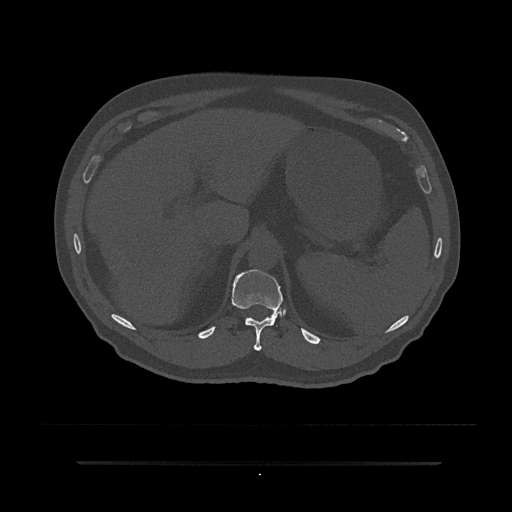
CT including the spine, one axial slice. Slice 260 of 797 in the series (ordered by position). Reconstruction kernel Br40s/3. 120 kVp. Bone window (W 1800 / L 400 HU). 512 × 512 image matrix, field of view 464 × 464 mm. Male patient, age 59 years. Case-level facts recorded for this patient, not image findings: primary cancer: bile ducts; vertebrae with lytic lesions (as recorded): T10.
Structures marked on this image (semi-automatic segmentation, software-assisted and operator-edited):
- T11 vertebra: bounding box (x1, y1, x2, y2) in pixels: (231, 269, 284, 351)